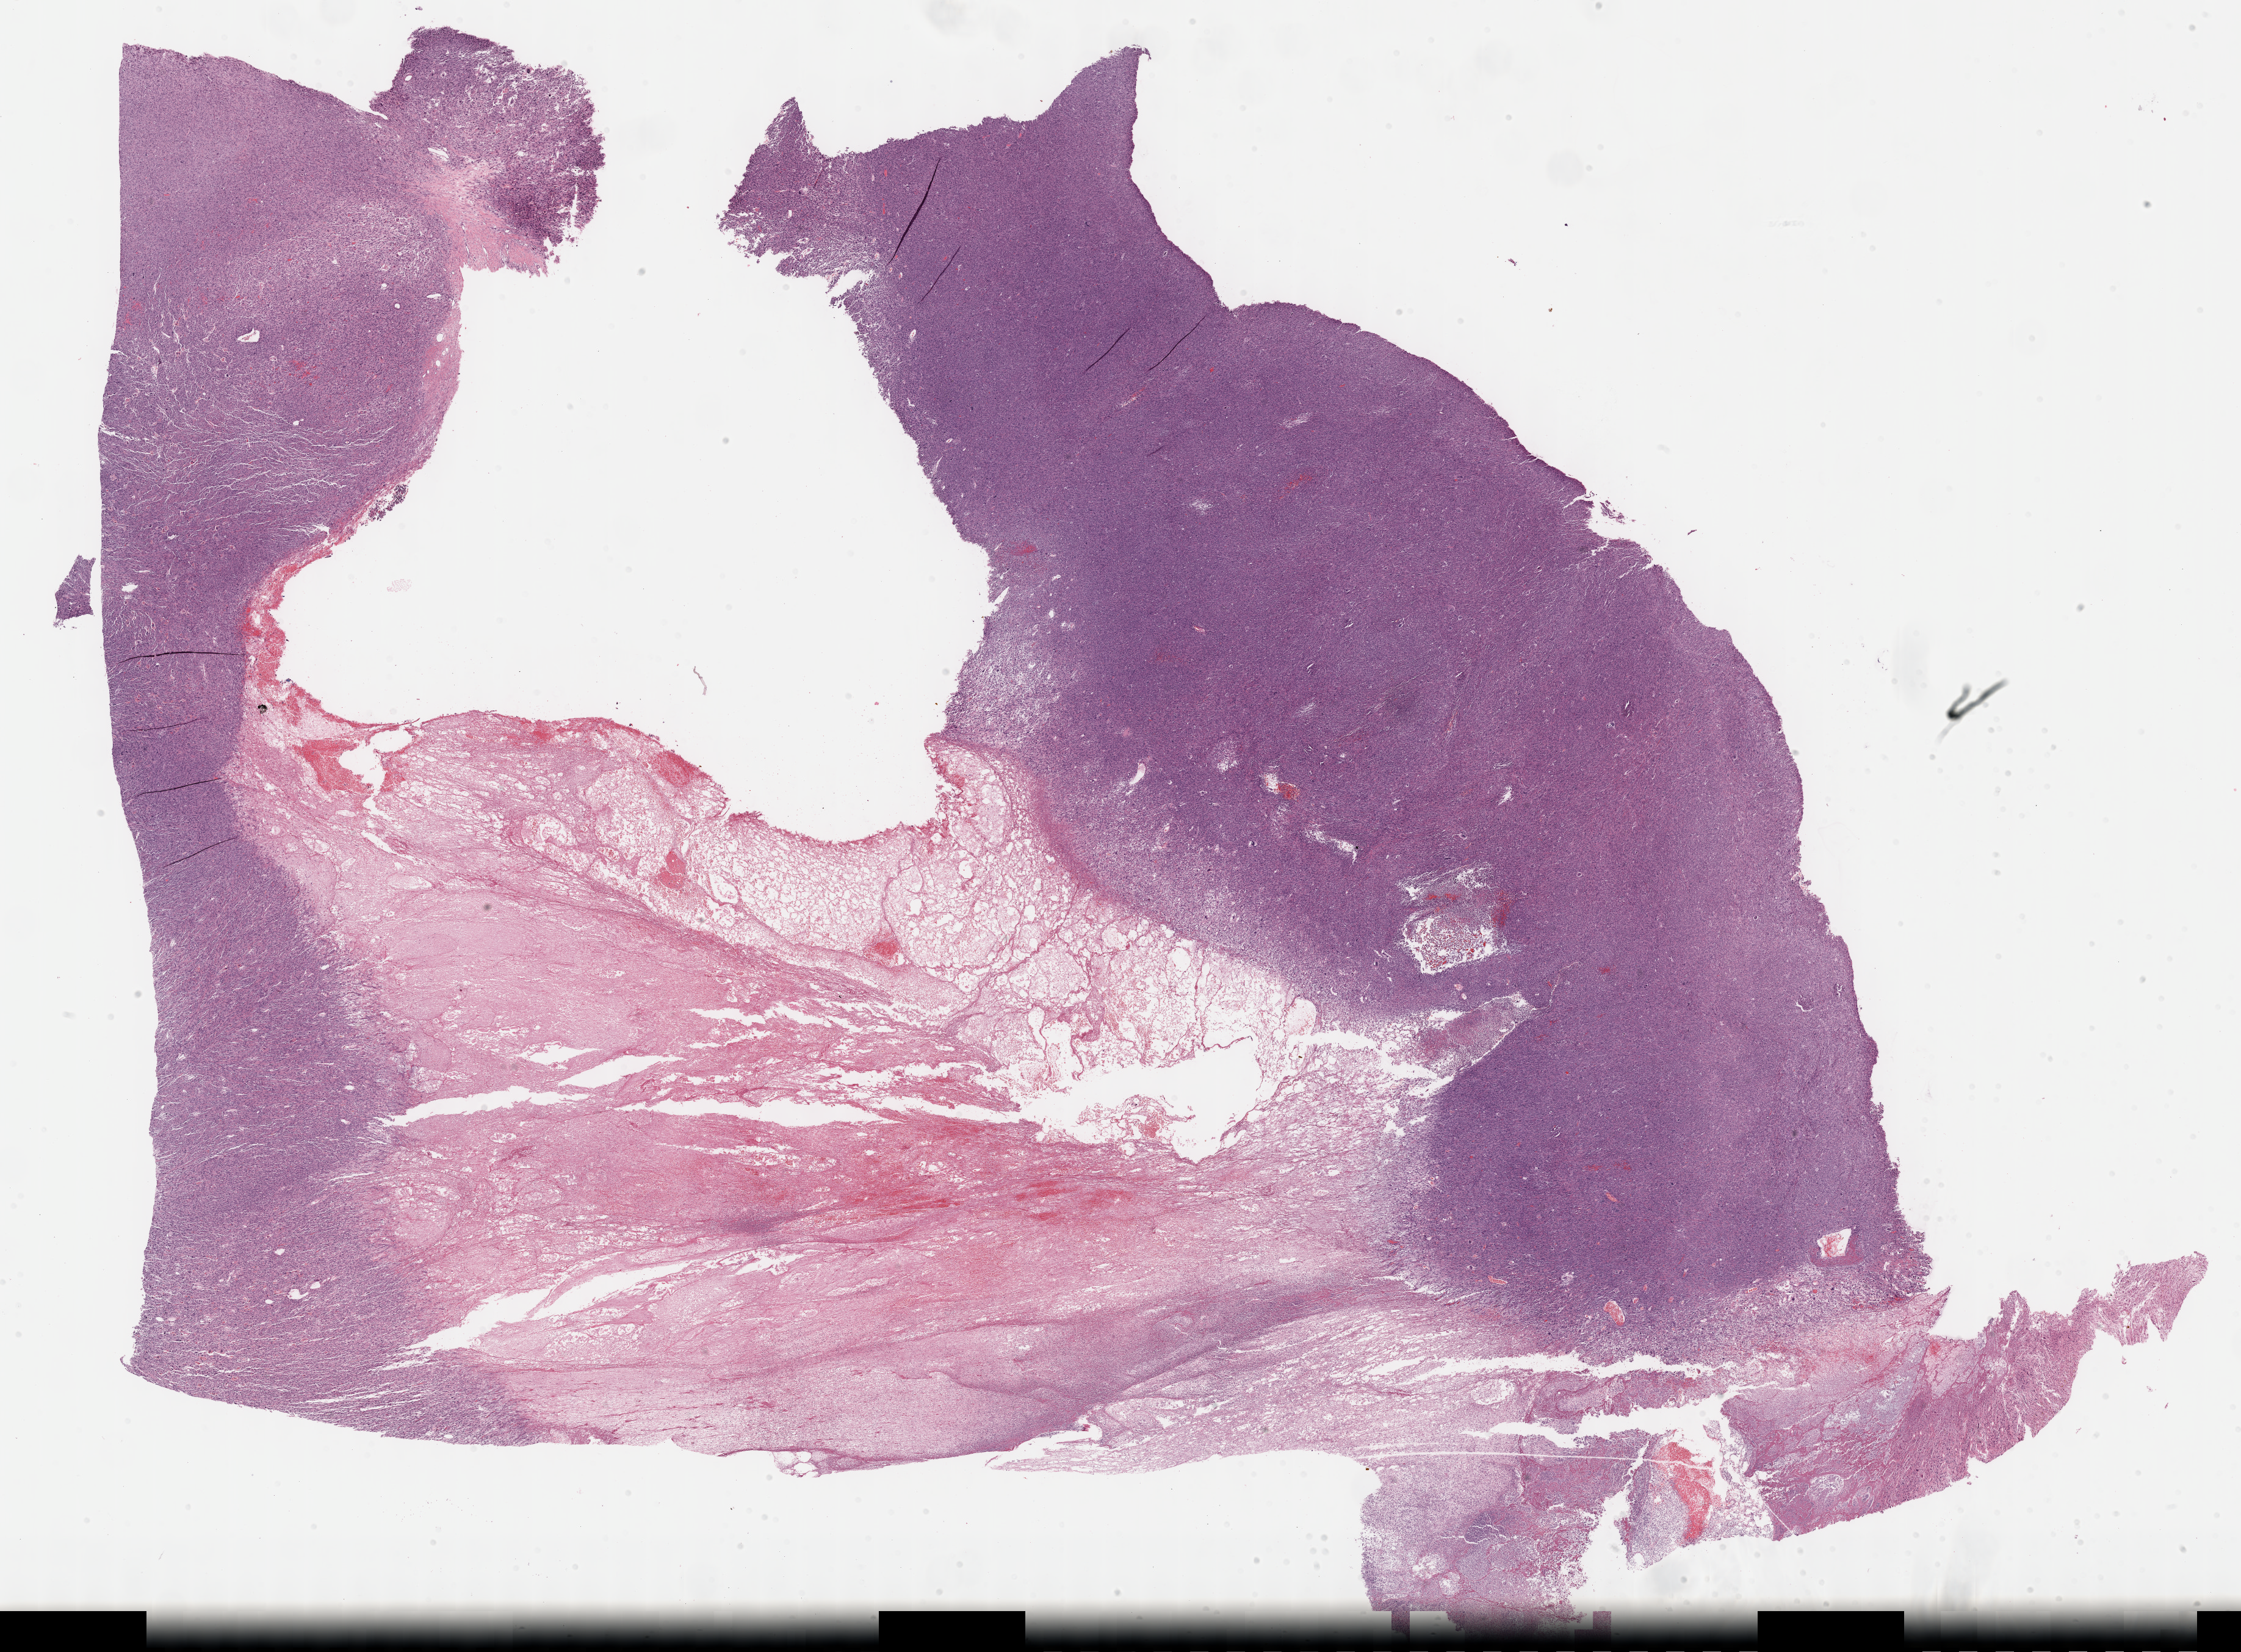
H&E-stained whole-slide image — low-resolution overview of the scanned area, about 29.7 x 21.9 mm, FFPE section, sample: primary tumour, connective, subcutaneous and other soft tissues. Male, age 79 years at initial diagnosis.
Diagnosis: Malignant fibrous histiocytoma (connective, subcutaneous and other soft tissues of lower limb and hip).